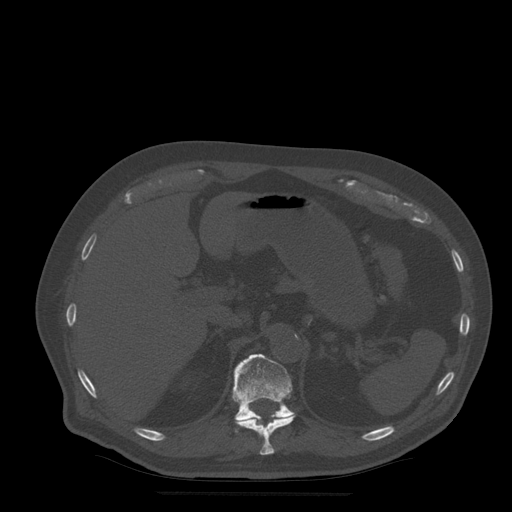
CT including the spine, one axial slice. Slice 232 of 522 in the series (ordered by position). Bone window (W 1800 / L 400 HU). 1.25 mm slice thickness. 512 × 512 image matrix. Patient age 72 years. Case-level facts recorded for this patient, not image findings: primary cancer: prostate.
Outlined on this slice (semi-automatic segmentation, software-assisted and operator-edited):
- T11 vertebra: bounding box (x1, y1, x2, y2) in pixels: (235, 413, 296, 456)
- T12 vertebra: (233, 354, 294, 433)